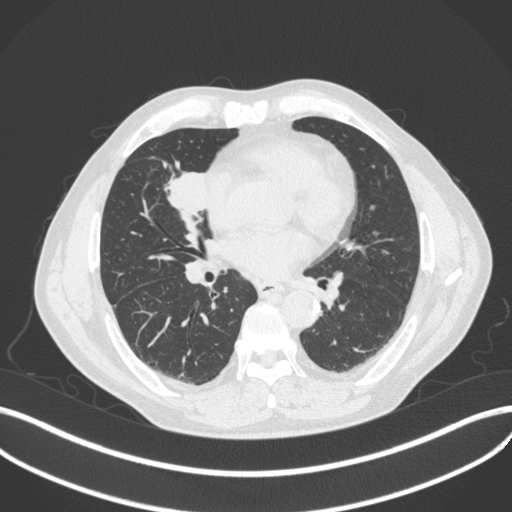
Chest CT, one axial slice; slice 190 of 429 in the series (ordered by position); 120 kVp; lung window (W 1500 / L -600 HU); 512 × 512 image matrix, field of view 400 × 400 mm. Patient: male, 61 years. Case-level facts recorded for this patient, not image findings: clinical TNM (as recorded): T2b N1 M0.
Annotated regions visible in this slice (rectangle marked by the reading radiologist):
- lung tumour (recorded histology: squamous cell carcinoma): bounding box (x1, y1, x2, y2) in pixels: (158, 161, 209, 222)